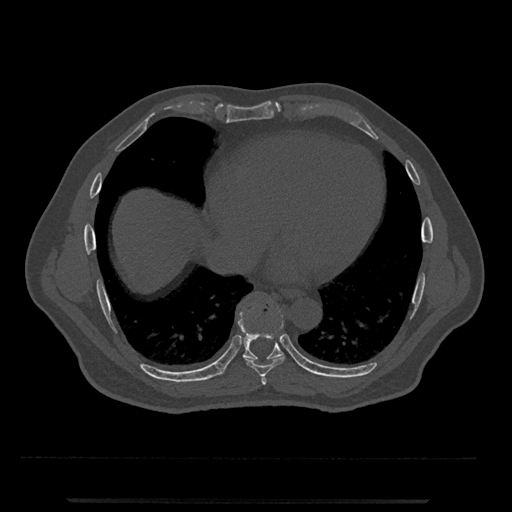
CT including the spine, one axial slice. Slice 603 of 797 in the series (ordered by position). Reconstruction kernel Br40s/3. 120 kVp. Bone window (W 1800 / L 400 HU). 0.5 mm slice thickness. 512 × 512 image matrix. Patient: male, 63 years. From the clinical record (not read from this slice): primary cancer: prostate.
Structures marked on this image (semi-automatic segmentation, software-assisted and operator-edited):
- T7 vertebra: box from (x=261, y=376) to (x=267, y=385) px
- T8 vertebra: (x=243, y=333)–(x=285, y=377)
- T9 vertebra: (x=222, y=298)–(x=284, y=374)